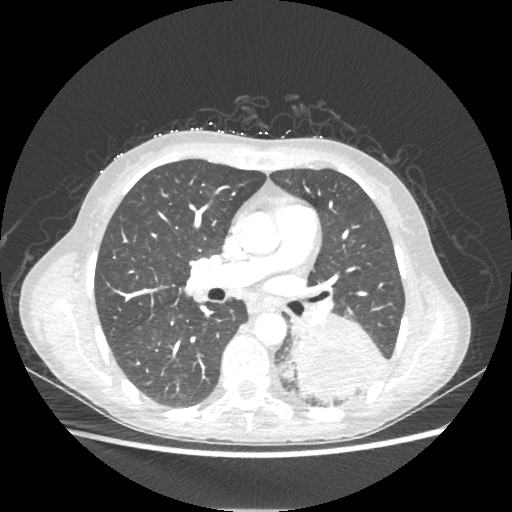
Chest CT, one axial slice. Slice 121 of 221 in the series (ordered by position). Reconstruction kernel STANDARD. 80 kVp. Lung window (W 1500 / L -600 HU). 512 × 512 image matrix, field of view 360 × 360 mm. Patient: female, 53 years. From the clinical record (not read from this slice): clinical TNM (as recorded): T3 N0 M0.
Annotated regions visible in this slice (rectangle marked by the reading radiologist):
- lung tumour (recorded histology: adenocarcinoma): bounding box (x1, y1, x2, y2) in pixels: (291, 300, 389, 403)